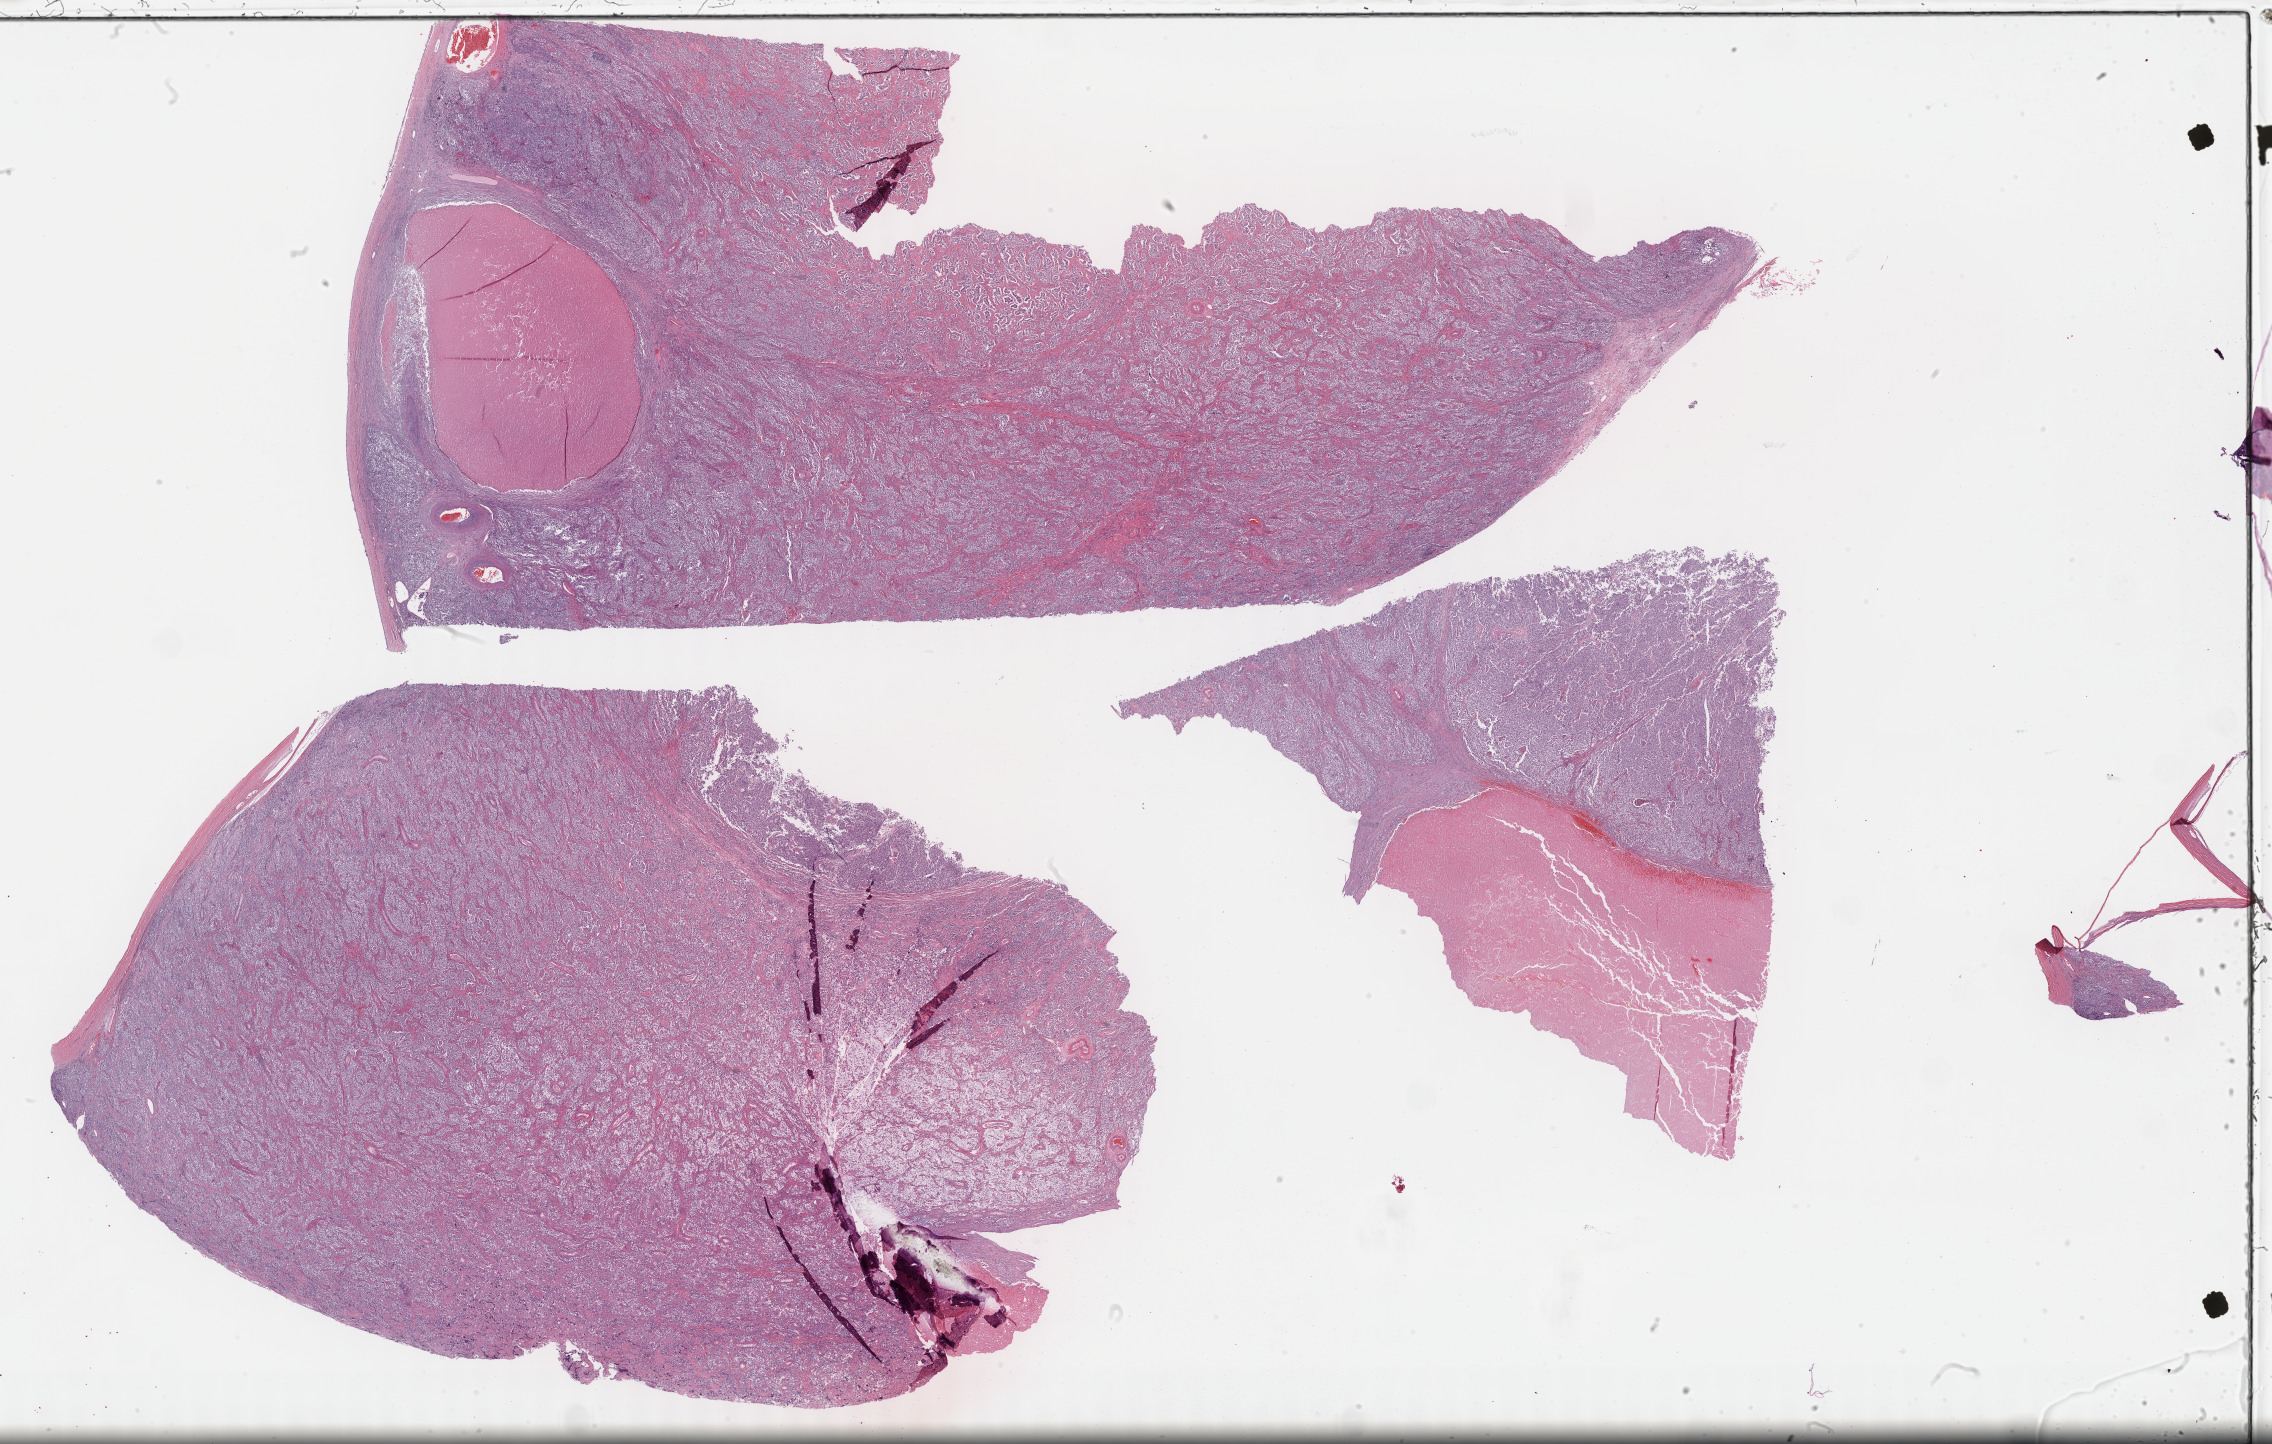
Whole-slide histology image, Hematoxylin and eosin (H&E) stained — a low-resolution overview of the entire scanned area, about 36.7 x 23.4 mm (acquisition: 40x scan), formalin-fixed paraffin-embedded (FFPE) diagnostic section, testis, primary tumour sample. Male patient; age at initial diagnosis 39 years.
• pathologic diagnosis: Seminoma, NOS
• TNM: T2 NX M0
• AJCC pathologic stage: IS (6th edition)
• laterality: left